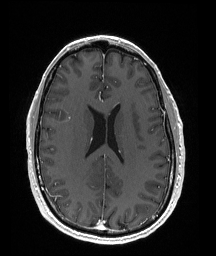
Brain MRI from a brain-tumour surgery series, one axial slice. Position 74 of 176 along the scan axis. T1-weighted post-contrast. 216 × 256 image matrix, field of view 211 × 250 mm. From the clinical record (not read from this slice): histopathology: Oligodendroglioma; WHO grade: 2; IDH mutation: yes; tumour location: Right Parietal.
Outlined on this slice (outlined manually by an expert reader):
- tumour: bounding box (x1, y1, x2, y2) in pixels: (70, 177, 111, 190)